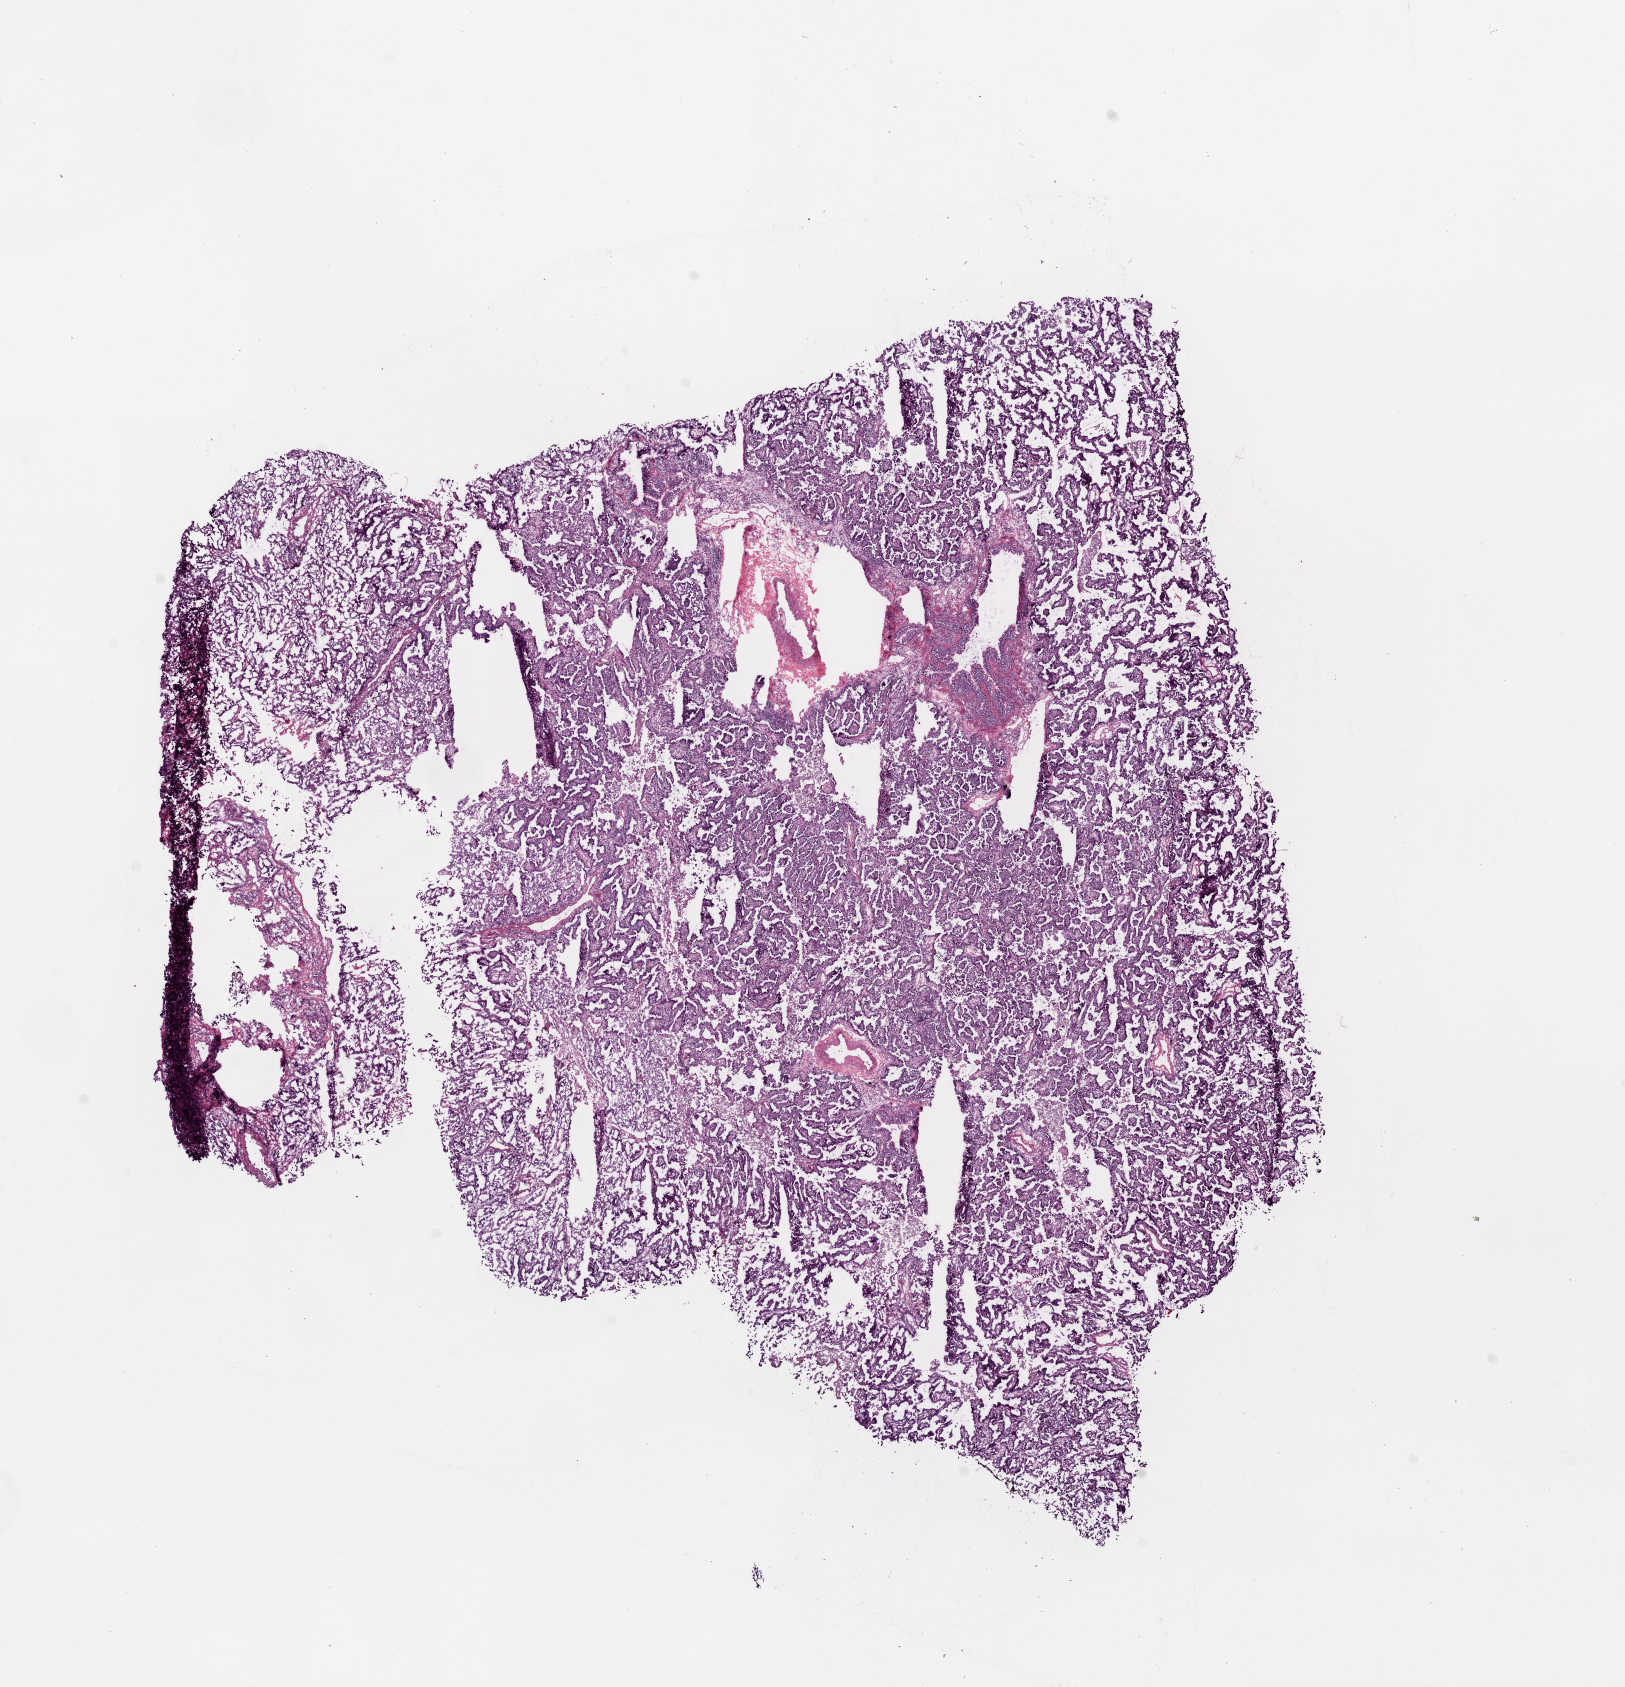
Digitized H&E tissue section (whole slide), shown as a low-resolution overview of the whole scanned area (about 13.0 x 13.5 mm, slide scanned at 20x), frozen section from the bottom of the tissue portion, lung, primary tumour sample. Female patient; age at initial diagnosis 51 years. Slide review estimates, as recorded: tumour cells 95%, tumour nuclei 75%, normal cells 0%, stromal cells 5%, necrosis 0%.
- pathologic diagnosis: Adenocarcinoma, NOS (upper lobe, lung)
- AJCC pathologic stage: IIB (5th edition)